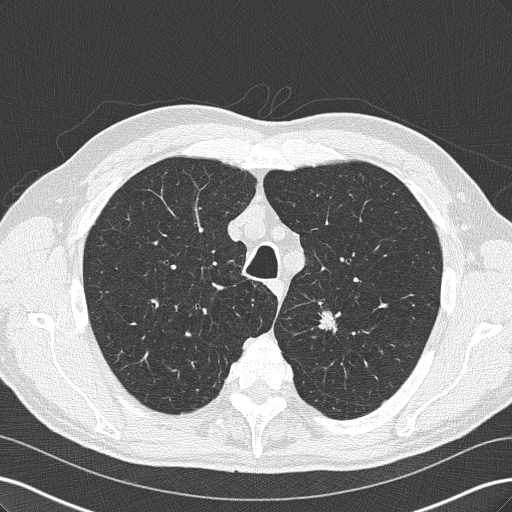
Low-dose screening chest CT, axial slice; third screening round (two years after baseline); lung window (W 1500 / L -600 HU); 2 mm slice thickness; lung (sharp) reconstruction kernel (B50f); 512 × 512 image matrix, field of view 360 × 360 mm. Male participant, aged 66 years at enrolment. Current smoker at enrolment.
Lesion marked by an expert reader, bounding box <299,302,352,347> (left, top, right, bottom; pixels). Screening reader's record for this exam (one nodule recorded; not confirmed to be the boxed lesion): non-calcified nodule or mass ≥4 mm, left upper lobe, 14 × 9 mm, spiculated (stellate) margins, soft tissue attenuation, pre-existing on the prior screen: yes; interval growth: yes. Official screen result: positive, other.